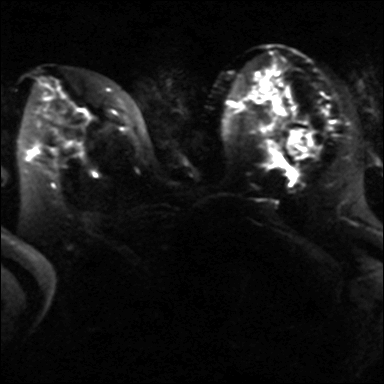
Breast MRI, one axial slice; position 21 of 40 along the scan axis; diffusion-weighted series; image 2 of 4 stored at this slice position (different b-values; order by instance number); 3 T; 4 mm slice thickness; 384 × 384 image matrix, field of view 320 × 320 mm. Female patient.
Structures marked on this image (manually delineated by an expert):
- tumour on diffusion-weighted imaging: bounding box [x1, y1, x2, y2] px = [287, 129, 313, 160]